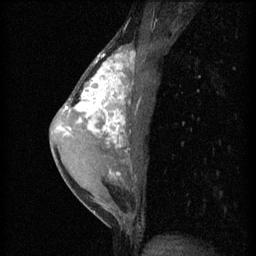
Breast MRI (dynamic contrast-enhanced), one sagittal slice. Slice 30 of 60 in the series (ordered by position). 3 images stored at this slice position (order not interpretable as contrast timing). 1.5 T. TE 4.2 ms, TR 11 ms. 2 mm slice thickness. 256 × 256 image matrix. Patient: female, 40 years.
Structures marked on this image (semi-automatic segmentation, software-assisted and operator-edited):
- analysis volume of interest (the breast-tissue region the enhancement analysis was run in; not a lesion): box from (x=55, y=44) to (x=143, y=203) px
- tumour enhancement mask (voxels above the 70 % enhancement threshold inside the analysis volume of interest): (x=60, y=48)–(x=136, y=175)